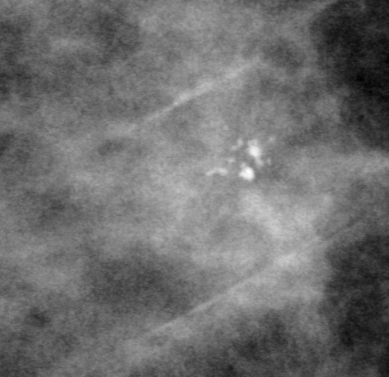
Crop from a digitized film mammogram around one marked abnormality; right breast; CC view.
Calcifications, morphology coarse, distribution clustered; BI-RADS assessment category 0 (incomplete: needs additional imaging); subtlety rating 5 on a 1 (subtle) to 5 (obvious) scale; pathology result (as recorded, not read from the image): benign.